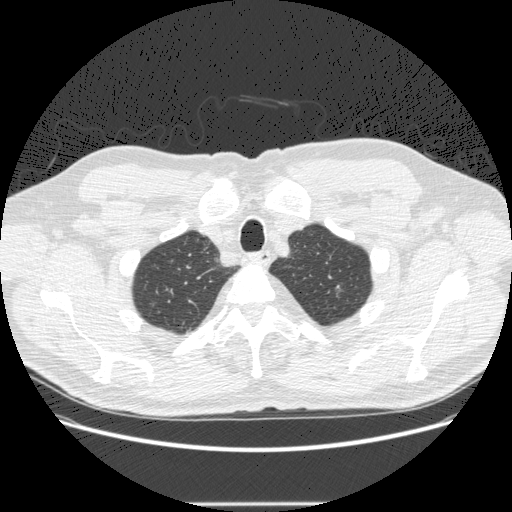
Low-dose screening chest CT, axial slice. Baseline annual screen. Lung window (W 1500 / L -600 HU). 1.25 mm slice thickness. Standard (soft-tissue) reconstruction kernel (STANDARD). 512 × 512 image matrix, field of view 389 × 389 mm. Male participant, aged 69 years at enrolment.
- Expert-annotated lung lesion, bounding box [x1, y1, x2, y2] px = [321, 276, 355, 303].
- Screening reader's record for this exam: no non-calcified nodule ≥4 mm recorded.